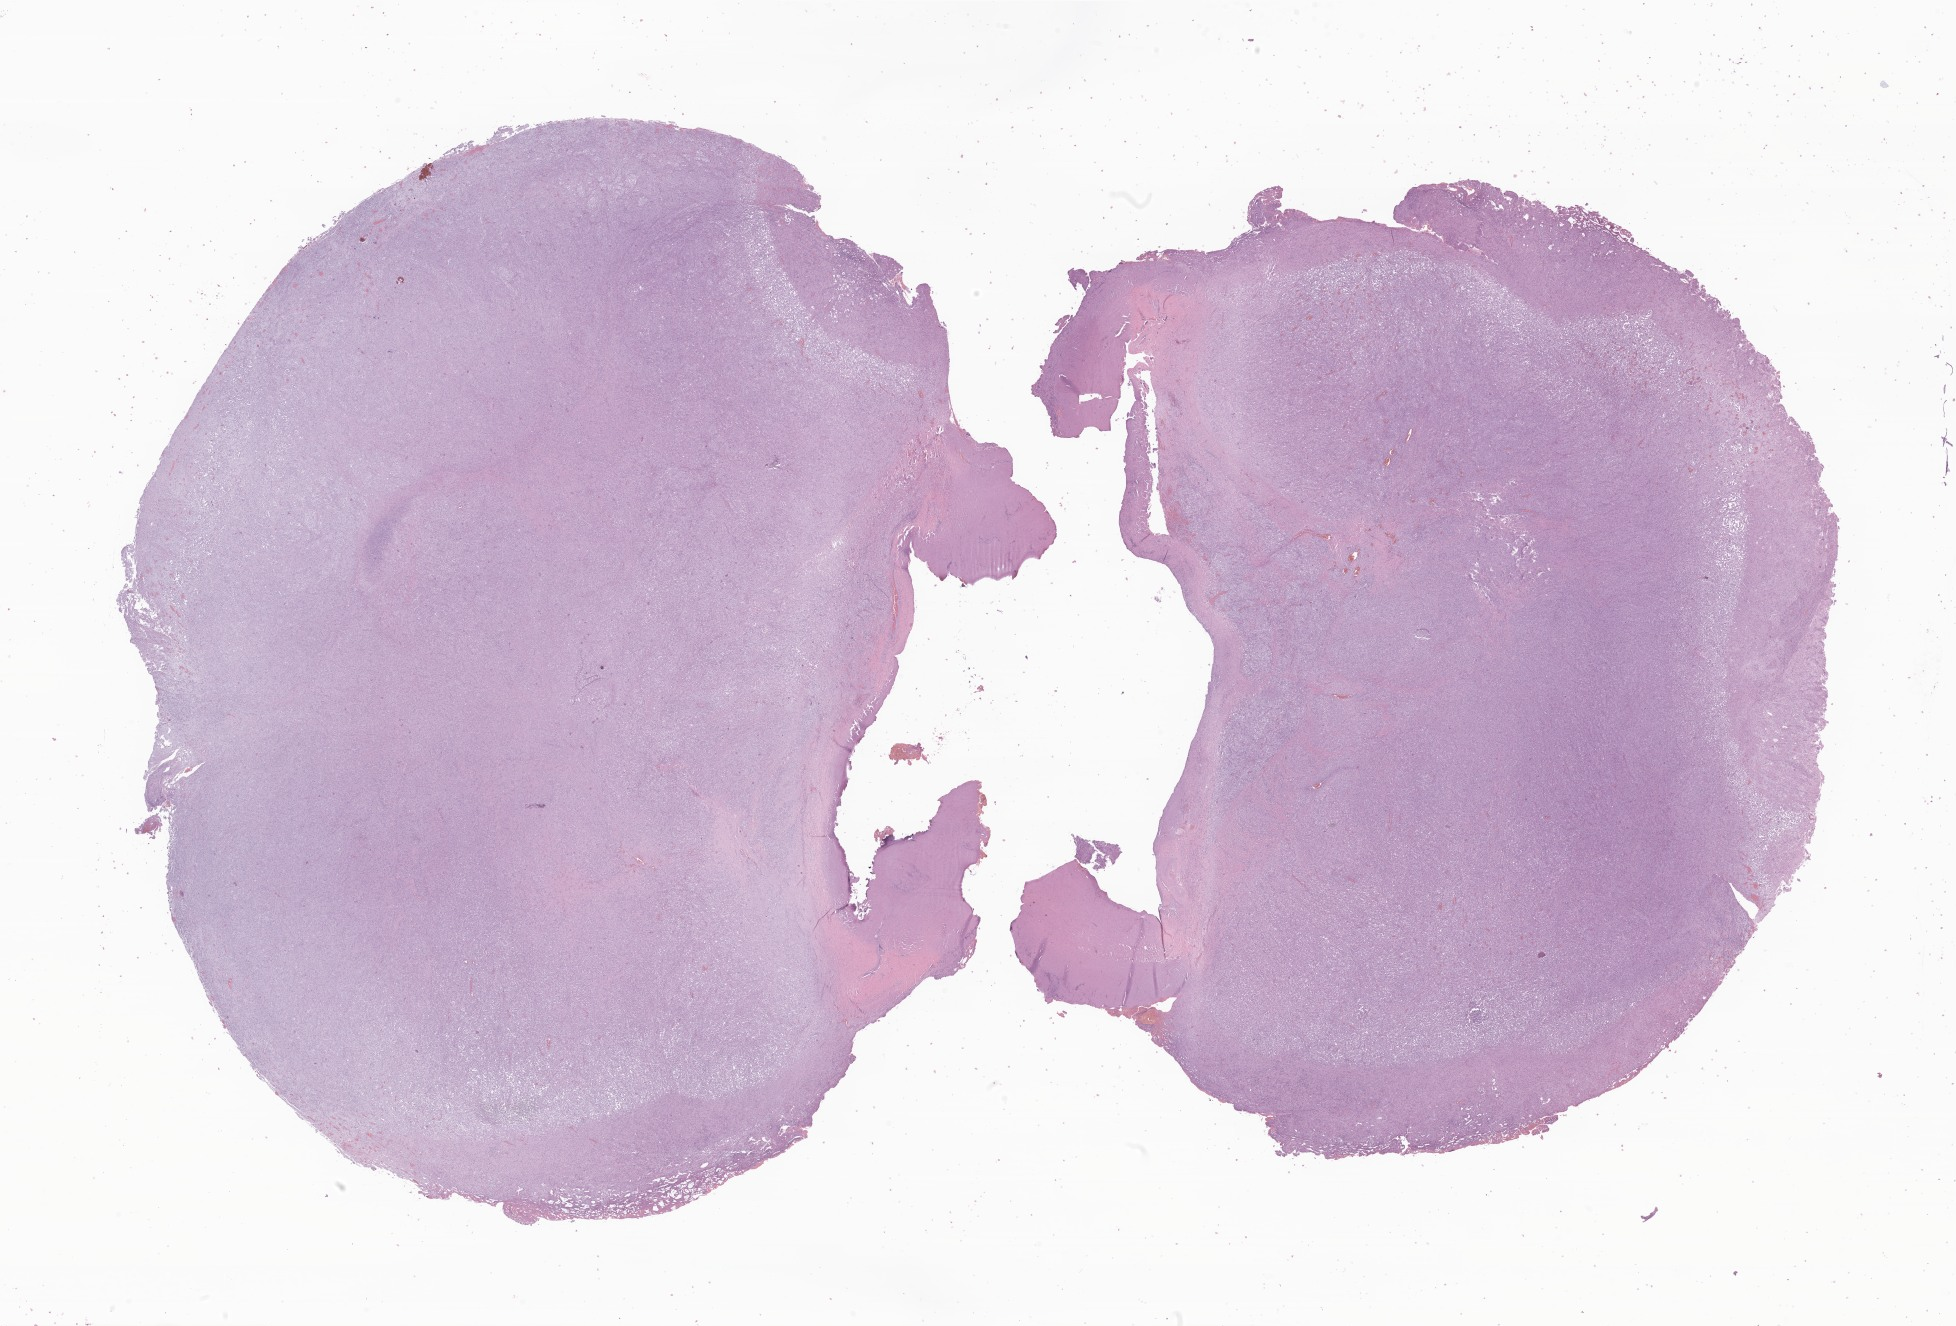
Hematoxylin and eosin (H&E) whole-slide image of tumor tissue from the brain, low-resolution overview of the scanned area, about 33.0 x 22.4 mm, FFPE section. Female patient, age 196 months (16 years 4 months).
Diagnosis (ICD-O-3 morphology term): Epithelioid sarcoma, NOS.